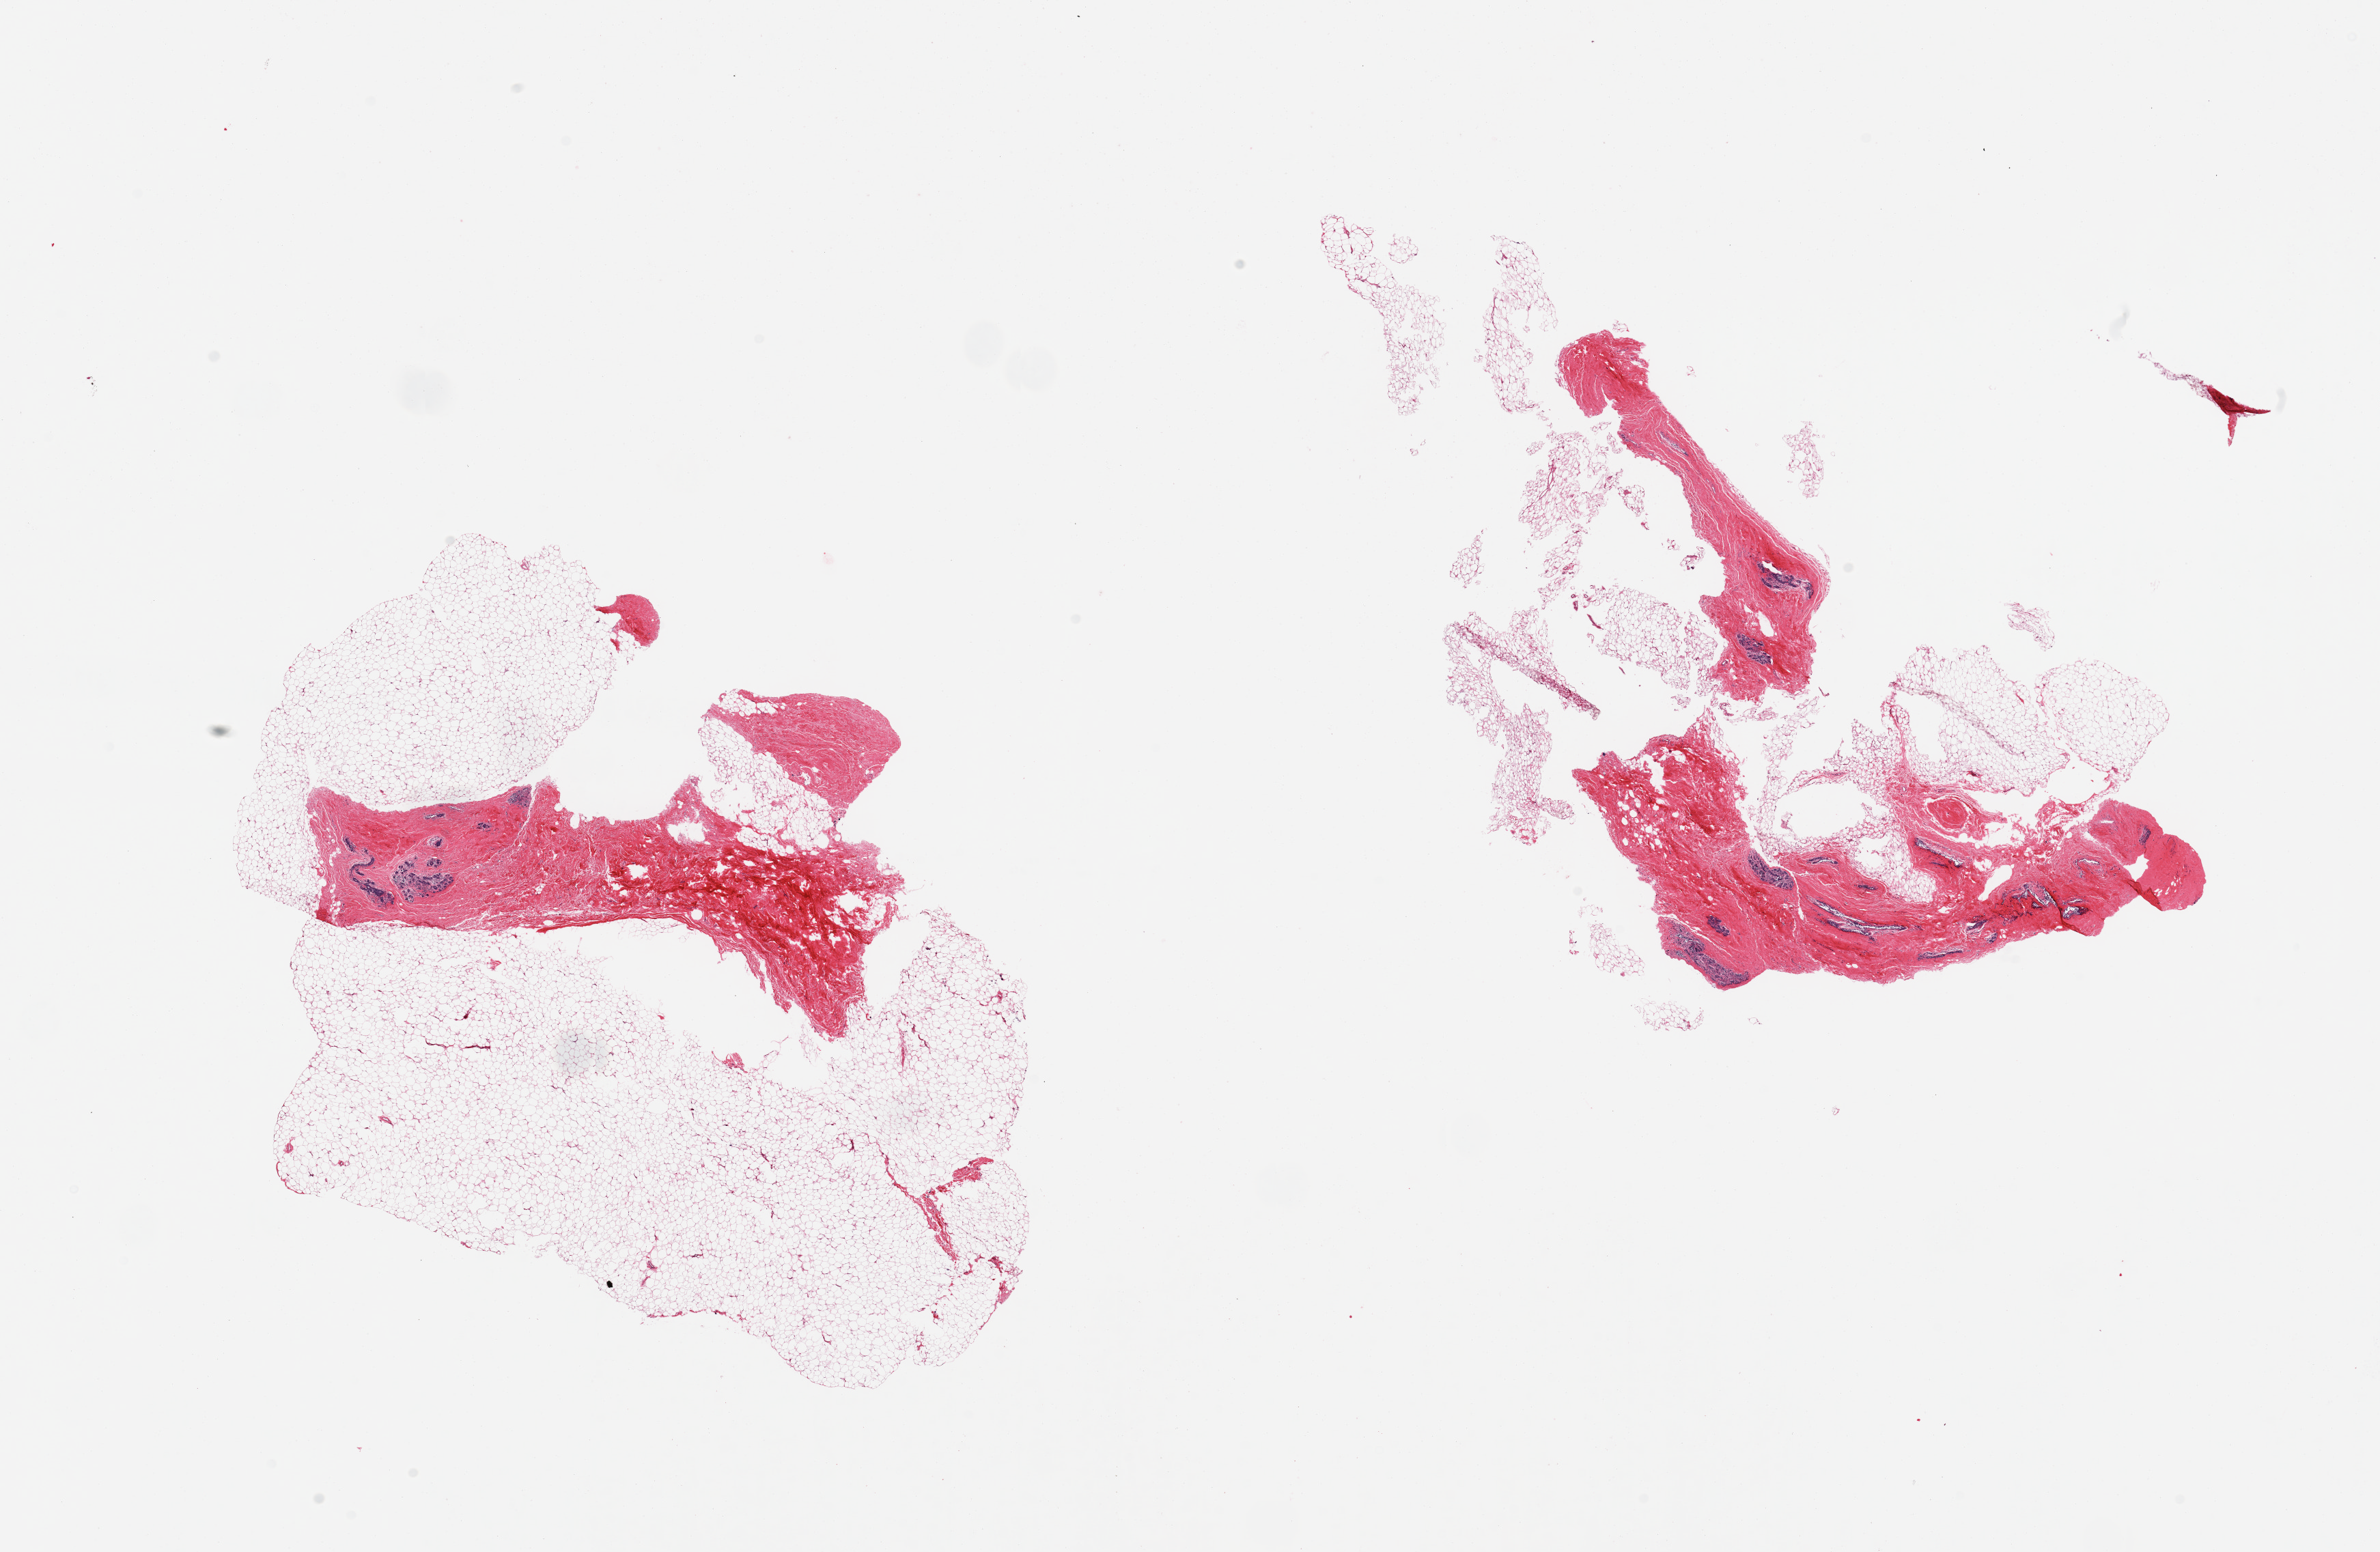
H&E whole-slide image — shown as a low-resolution overview of the whole scanned area (about 27.6 x 18.0 mm), PAXgene-fixed, paraffin-embedded tissue, sampled site (target tissue): breast, donor tissue sample. Female donor.
• reviewer comment on this tissue sample: 2 pieces; inactive ductal -lobular units